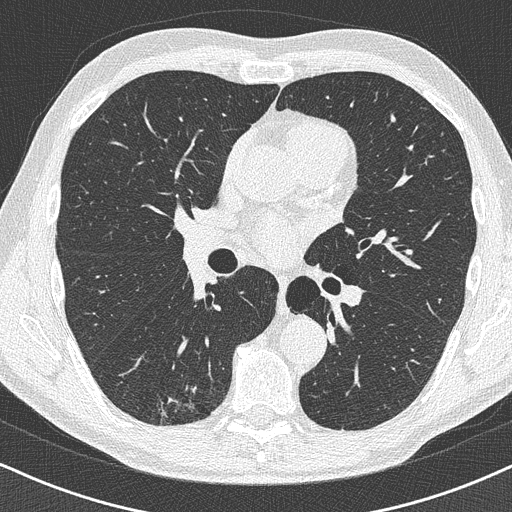
Axial slice from a low-dose chest CT screening exam; baseline screening round; lung window (W 1500 / L -600 HU); 1 mm slice thickness; 512 × 512 image matrix, field of view 320 × 320 mm. Male, age 63 years at enrolment. Former smoker at enrolment.
- Lesion marked by an expert reader, bounding box (x1, y1, x2, y2) in pixels: (141, 378, 213, 432).
- The exam's reader record, not a measurement of the box and not confirmed to be the same lesion: non-calcified nodule or mass ≥4 mm, right lower lobe, 16 × 13 mm, poorly defined margins.
- Lung cancer was diagnosed 74 days after this screen: adenocarcinoma, NOS, right lower lobe, moderately differentiated (G2), stage IA (AJCC 6th edition), 20 mm at pathology.